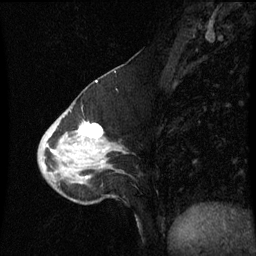
Breast MRI (dynamic contrast-enhanced), one sagittal slice; position 25 of 60 along the scan axis; dynamic contrast-enhanced series, image 2 of 3 at this slice position (ordered by acquisition); 1.5 T; TE 4.2 ms, TR 8.9 ms; 256 × 256 image matrix, field of view 200 × 200 mm. Female patient, age 50 years. From the clinical record (not read from this slice): setting: breast cancer imaged before/during neoadjuvant chemotherapy; receptor status: HR-positive, HER2-negative.
Structures marked on this image (semi-automatically segmented with operator editing):
- analysis volume of interest (the breast-tissue region the enhancement analysis was run in; not a lesion): box from (x=39, y=100) to (x=126, y=205) px
- tumour enhancement mask (voxels above the 70 % enhancement threshold inside the analysis volume of interest): (x=79, y=124)–(x=104, y=139)